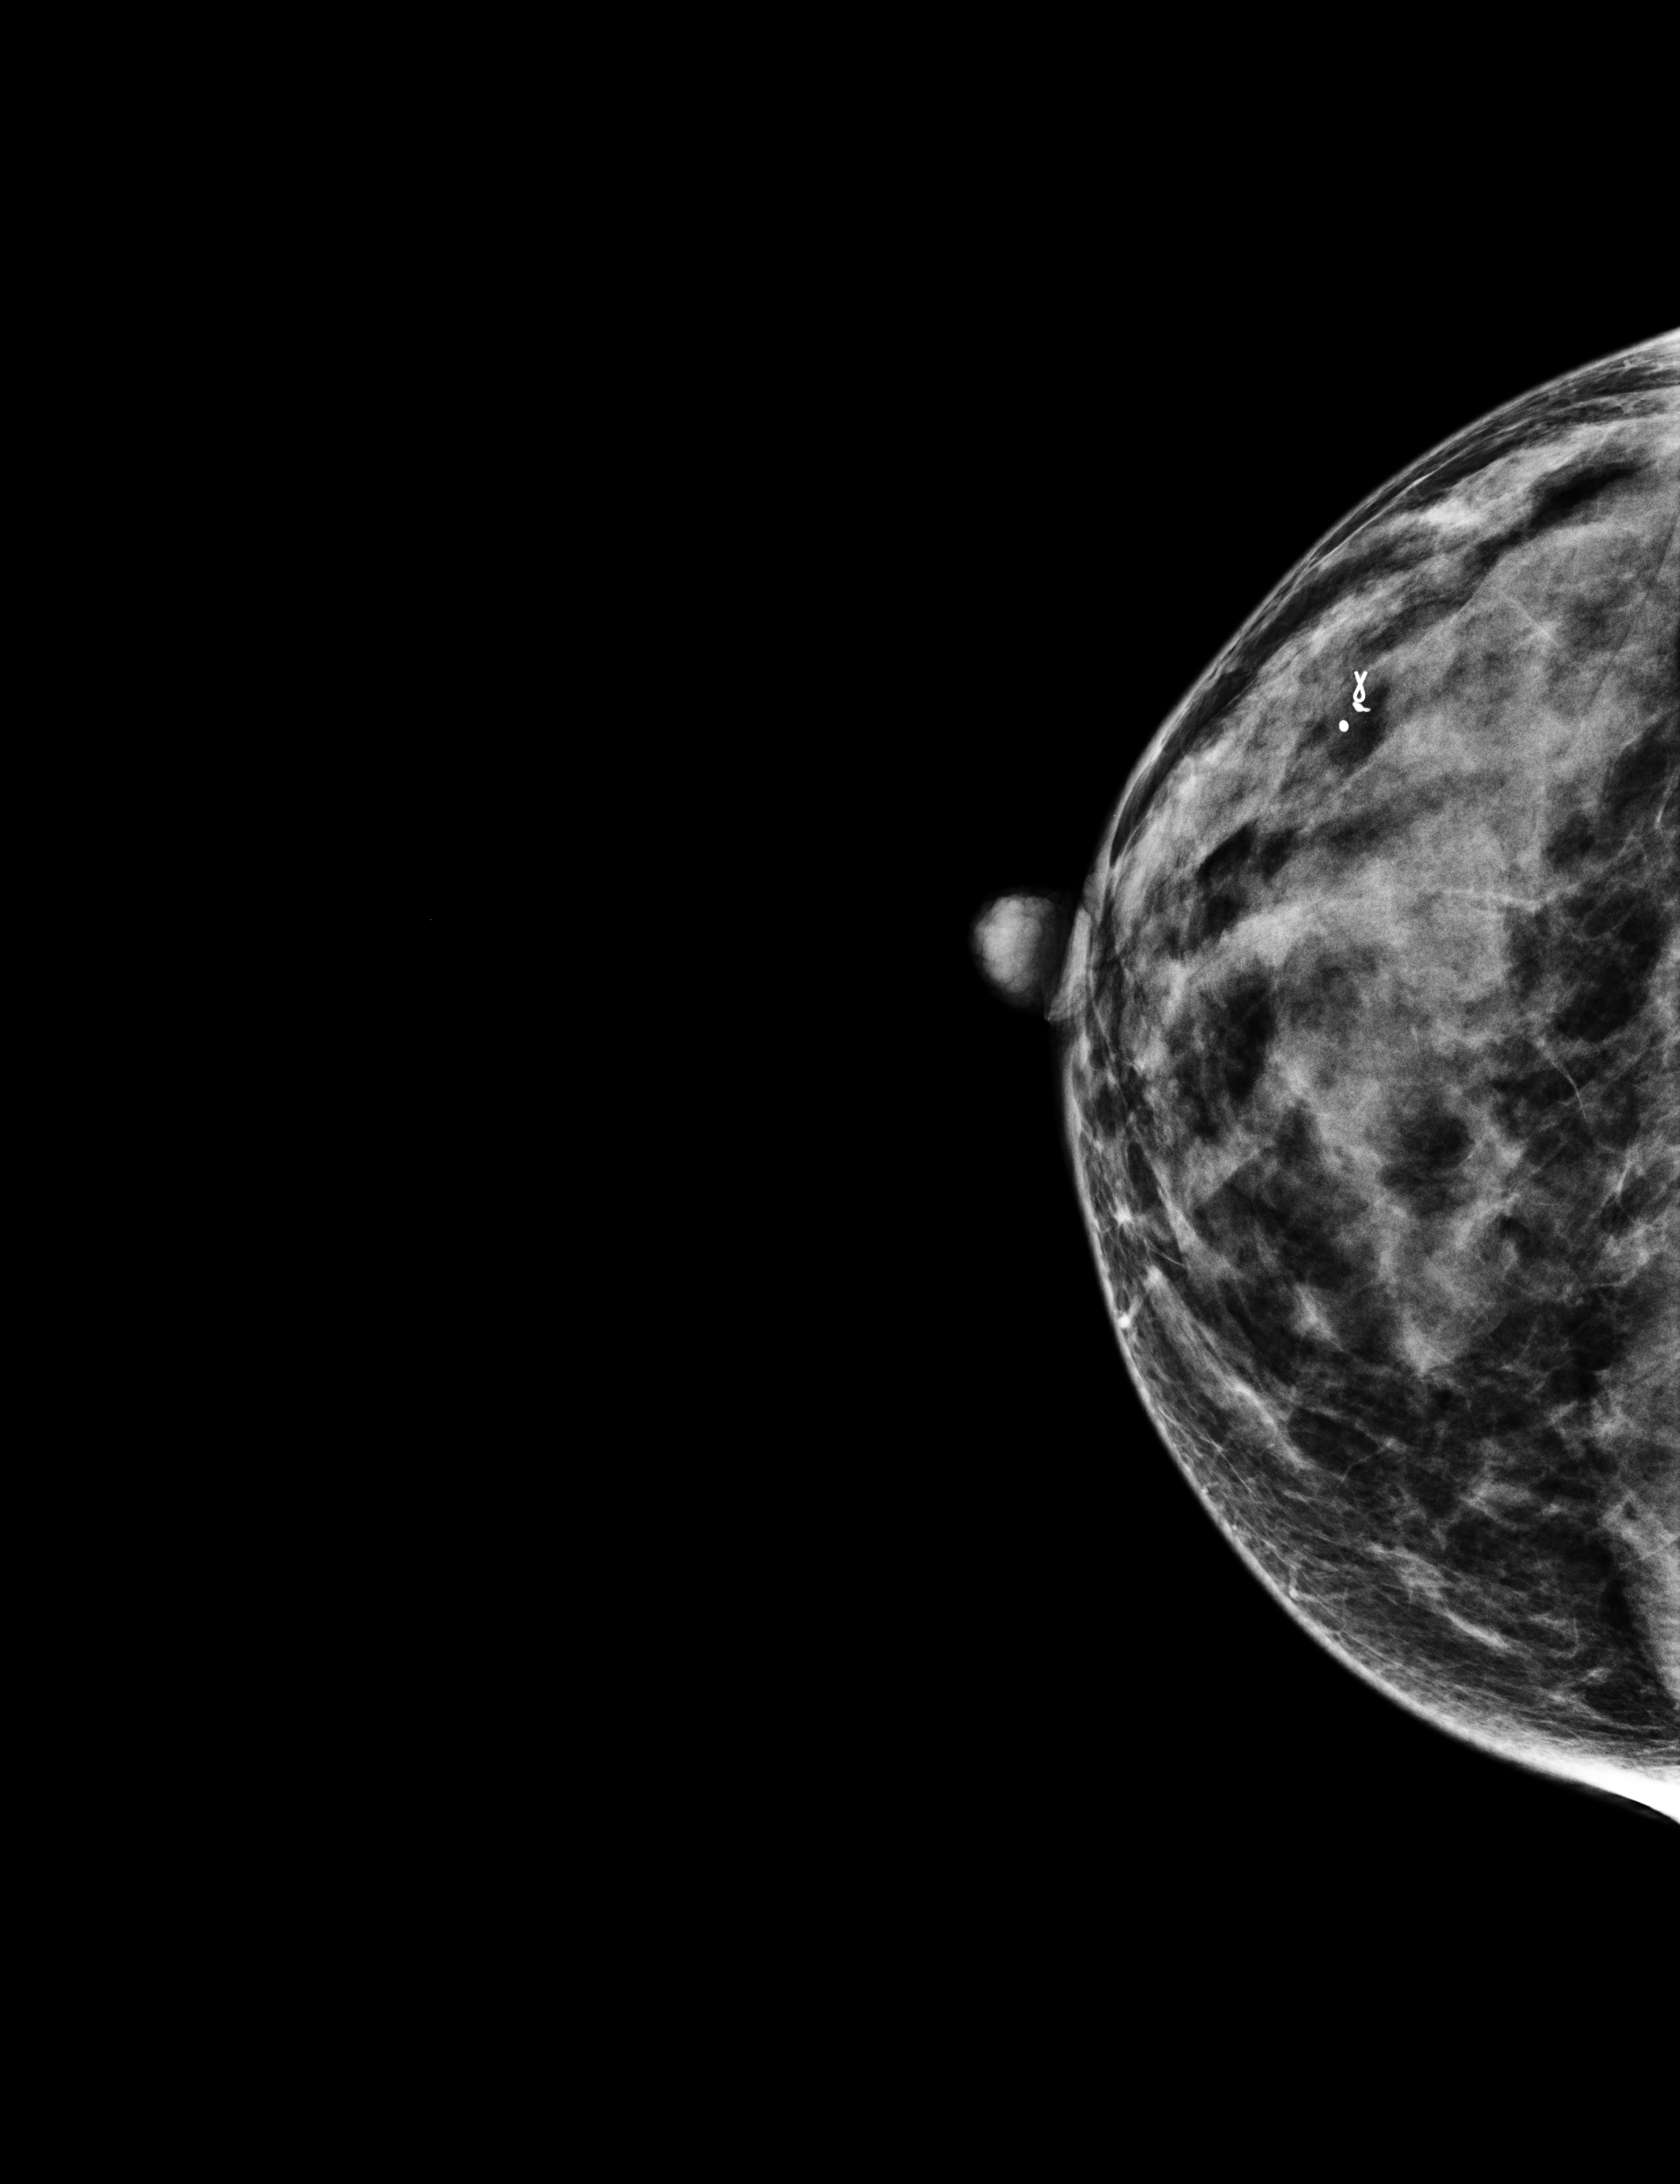
Screening examination. Patient: female, 54 years.
Image type: full-field digital mammogram. Breast: right. Projection: cranio-caudal projection.